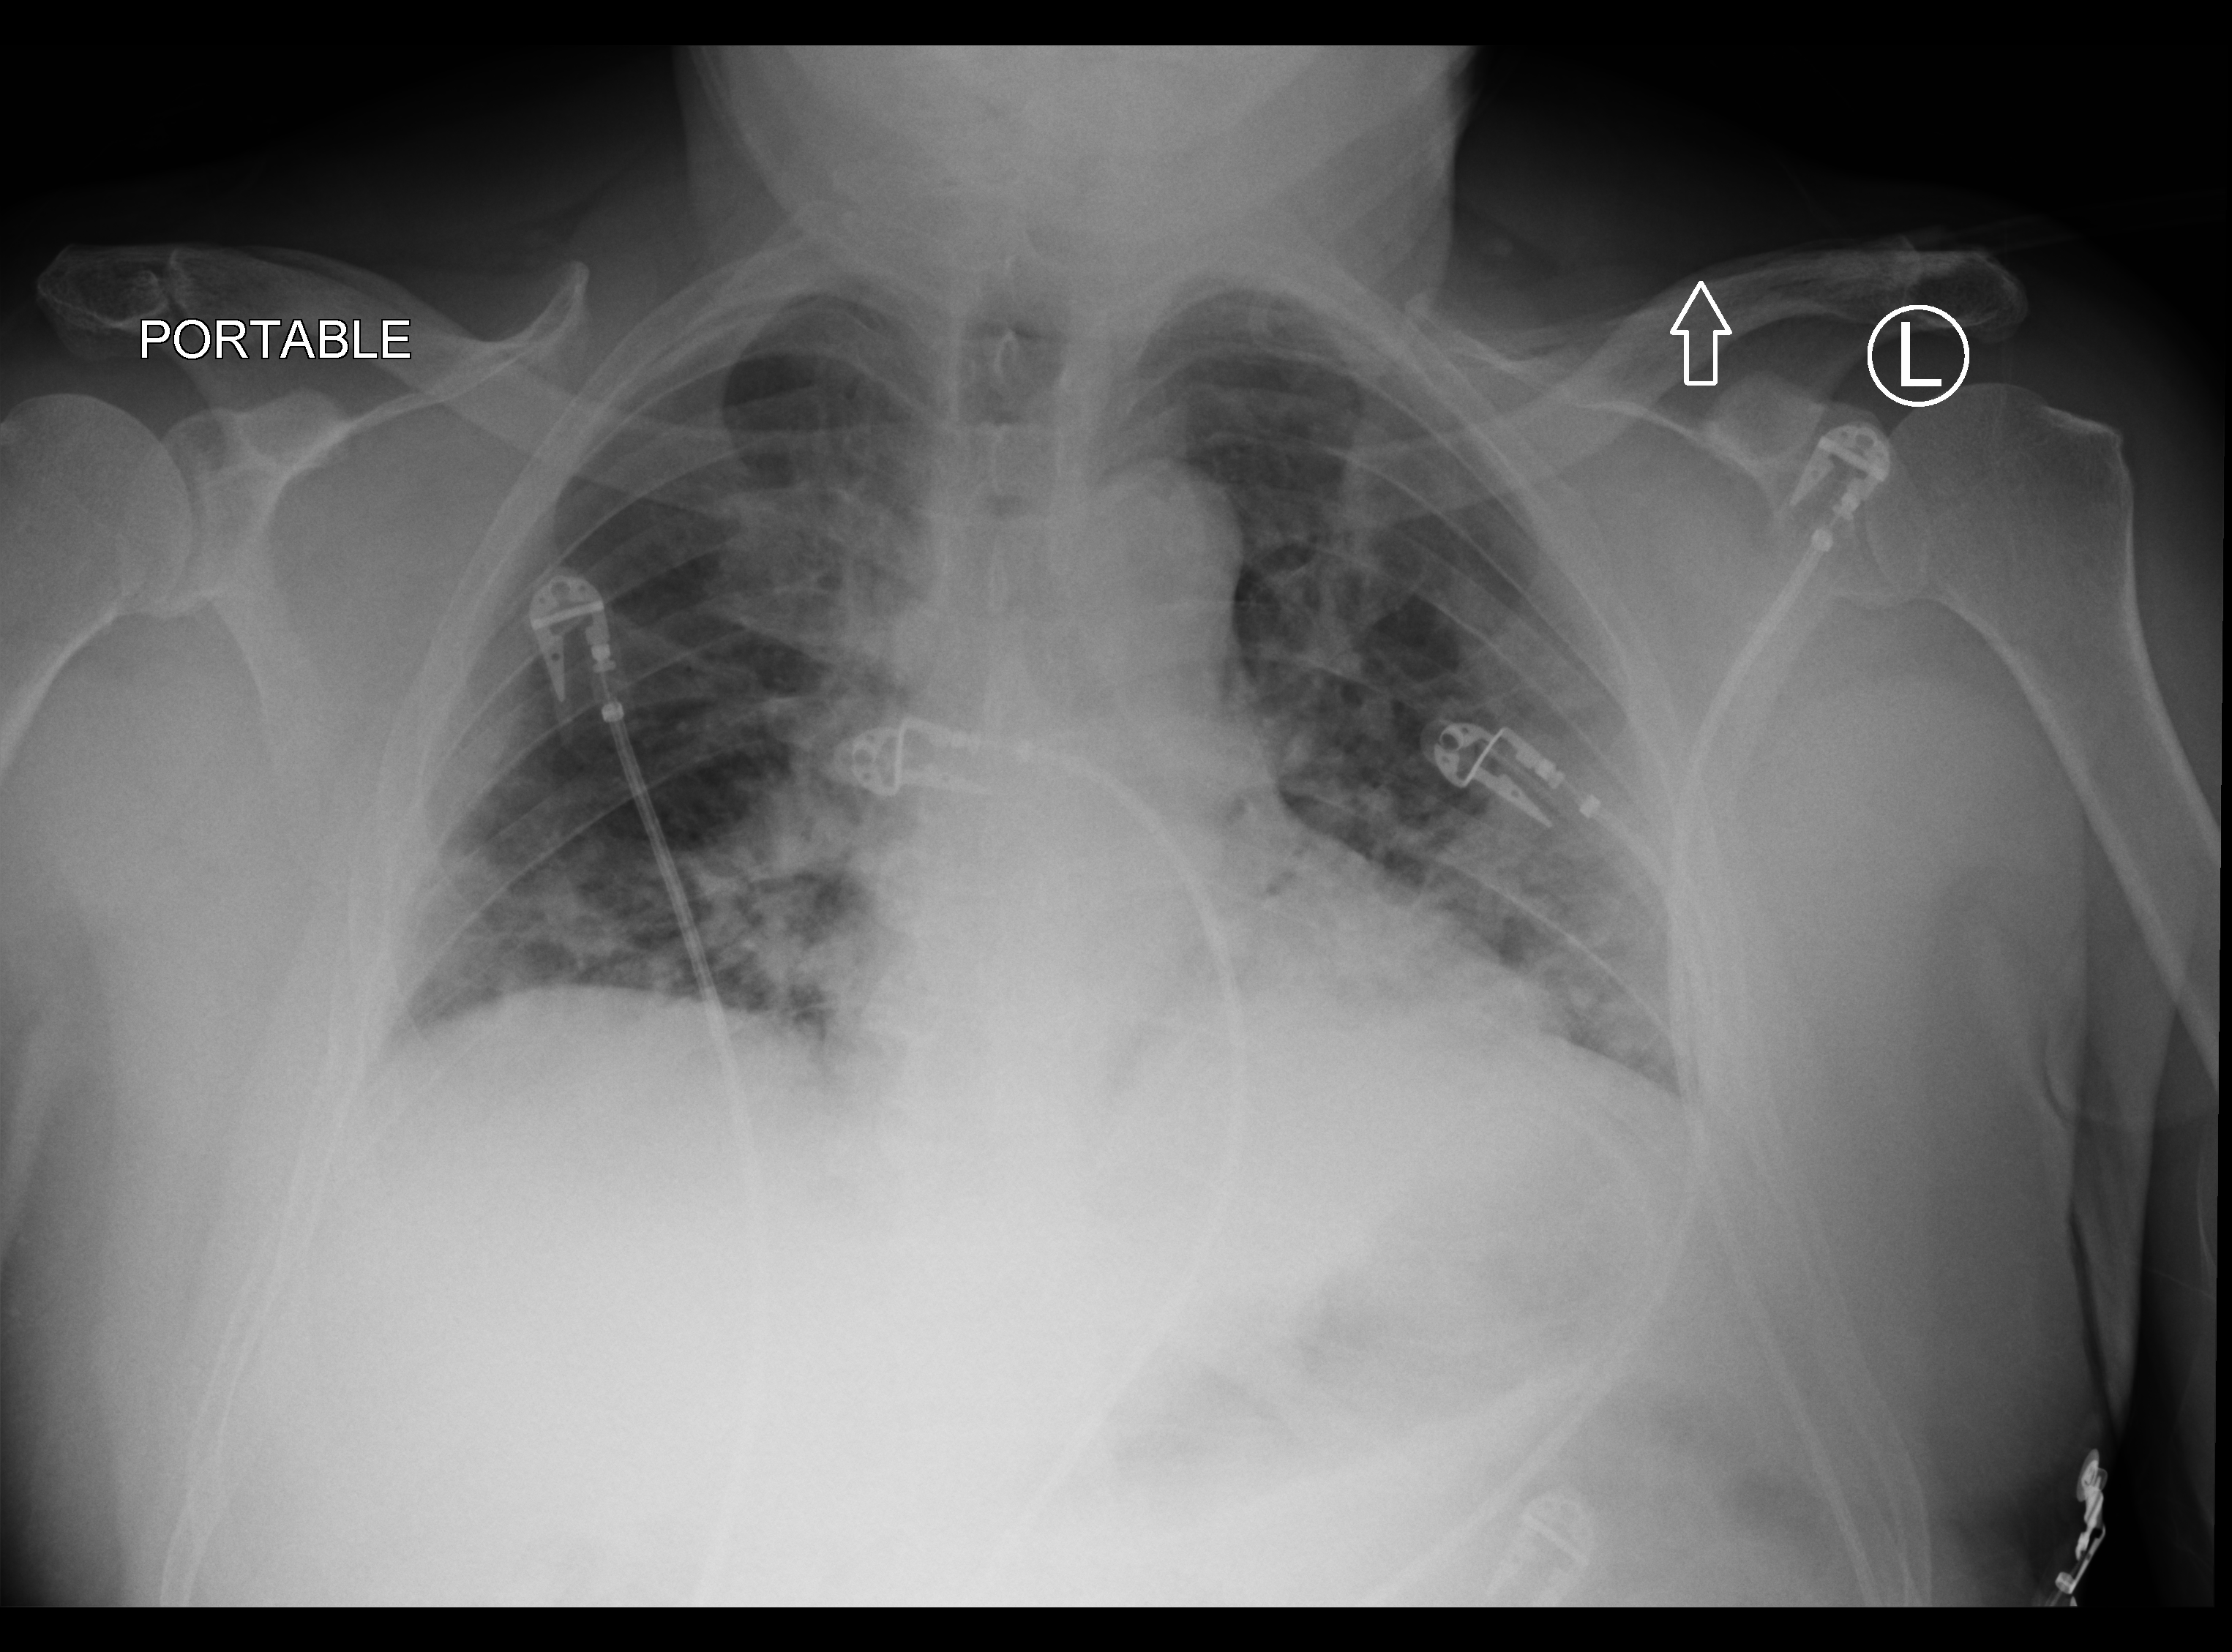
Chest X-ray (portable); anteroposterior (AP) projection. Patient hospitalised with COVID-19; male, aged 60–74 years.
Admission-level facts for this patient (not findings on this image; timing relative to this image not recorded):
- other chronic lung disease (admission record): no
- COPD (admission record): no
- mechanically ventilated during this hospital stay: no